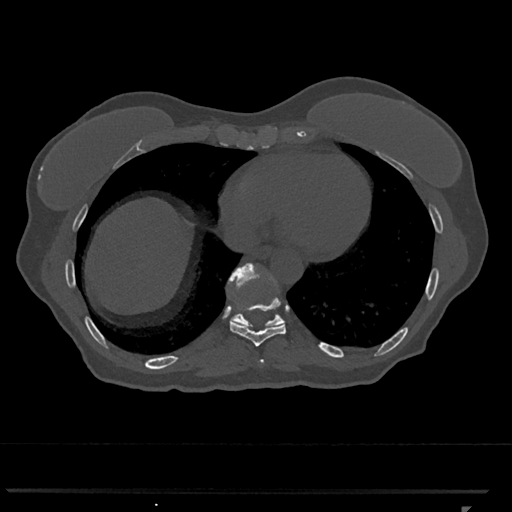
CT including the spine, one axial slice; slice 606 of 793 in the series (ordered by position); reconstruction kernel Br40s/3; 120 kVp; bone window (W 1800 / L 400 HU); 0.5 mm slice thickness; 512 × 512 image matrix, field of view 380 × 380 mm. Patient: female, 62 years. From the clinical record (not read from this slice): primary cancer: renal.
Structures marked on this image (semi-automatic segmentation, software-assisted and operator-edited):
- T10 vertebra: bounding box [x1, y1, x2, y2] px = [228, 263, 285, 327]
- T8 vertebra: [260, 359, 264, 363]
- T9 vertebra: [230, 298, 286, 347]